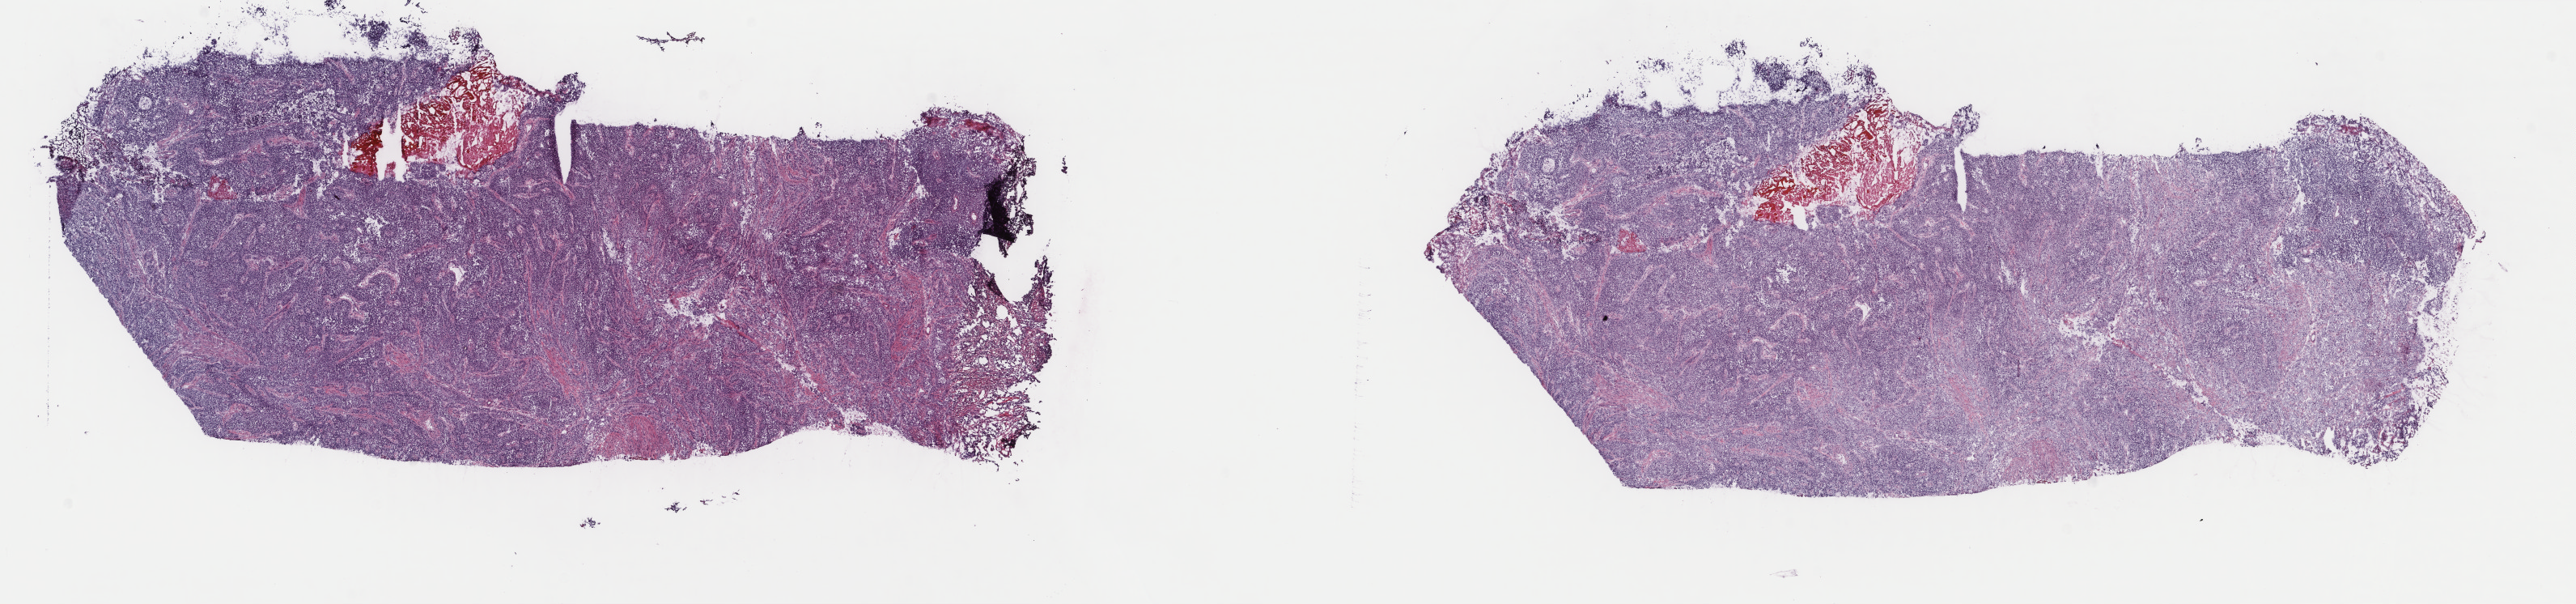
Whole-slide histology image, H&E — low-resolution overview of the scanned area, about 25.3 x 5.9 mm. Frozen section from the top of the tissue portion. Primary tumour sample from the bladder. Male patient; age at initial diagnosis 64 years. Histologic grade: high grade. Composition of this section per pathologist review: tumour cells 87%, tumour nuclei 75%, normal cells 0%, stromal cells 0%, necrosis 13%. Infiltration values recorded for this section: lymphocyte infiltration 4%, monocyte infiltration 0%, neutrophil infiltration 0%.
Histologic diagnosis: Transitional cell carcinoma. TNM: T3a N0 MX. AJCC pathologic stage: III.